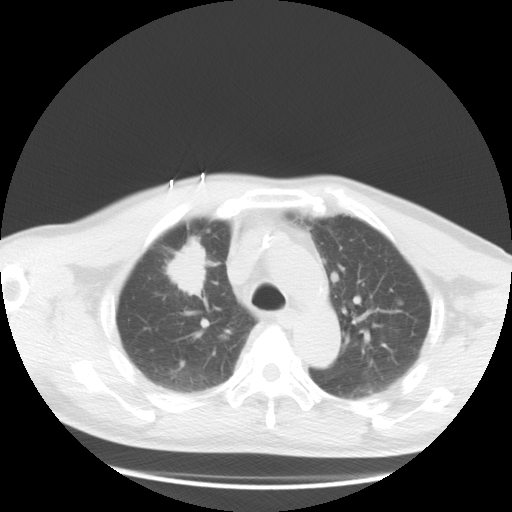
Chest CT, one axial slice; slice 22 of 36 in the series (ordered by position); reconstruction kernel STANDARD; 120 kVp; lung window (W 1500 / L -600 HU); 512 × 512 image matrix. Patient: male, 57 years. Case-level facts recorded for this patient, not image findings: clinical TNM (as recorded): T2 N3 M1a.
Outlined on this slice (bounding box drawn by a radiologist):
- lung tumour (recorded histology: adenocarcinoma): box from (x=163, y=237) to (x=208, y=301) px